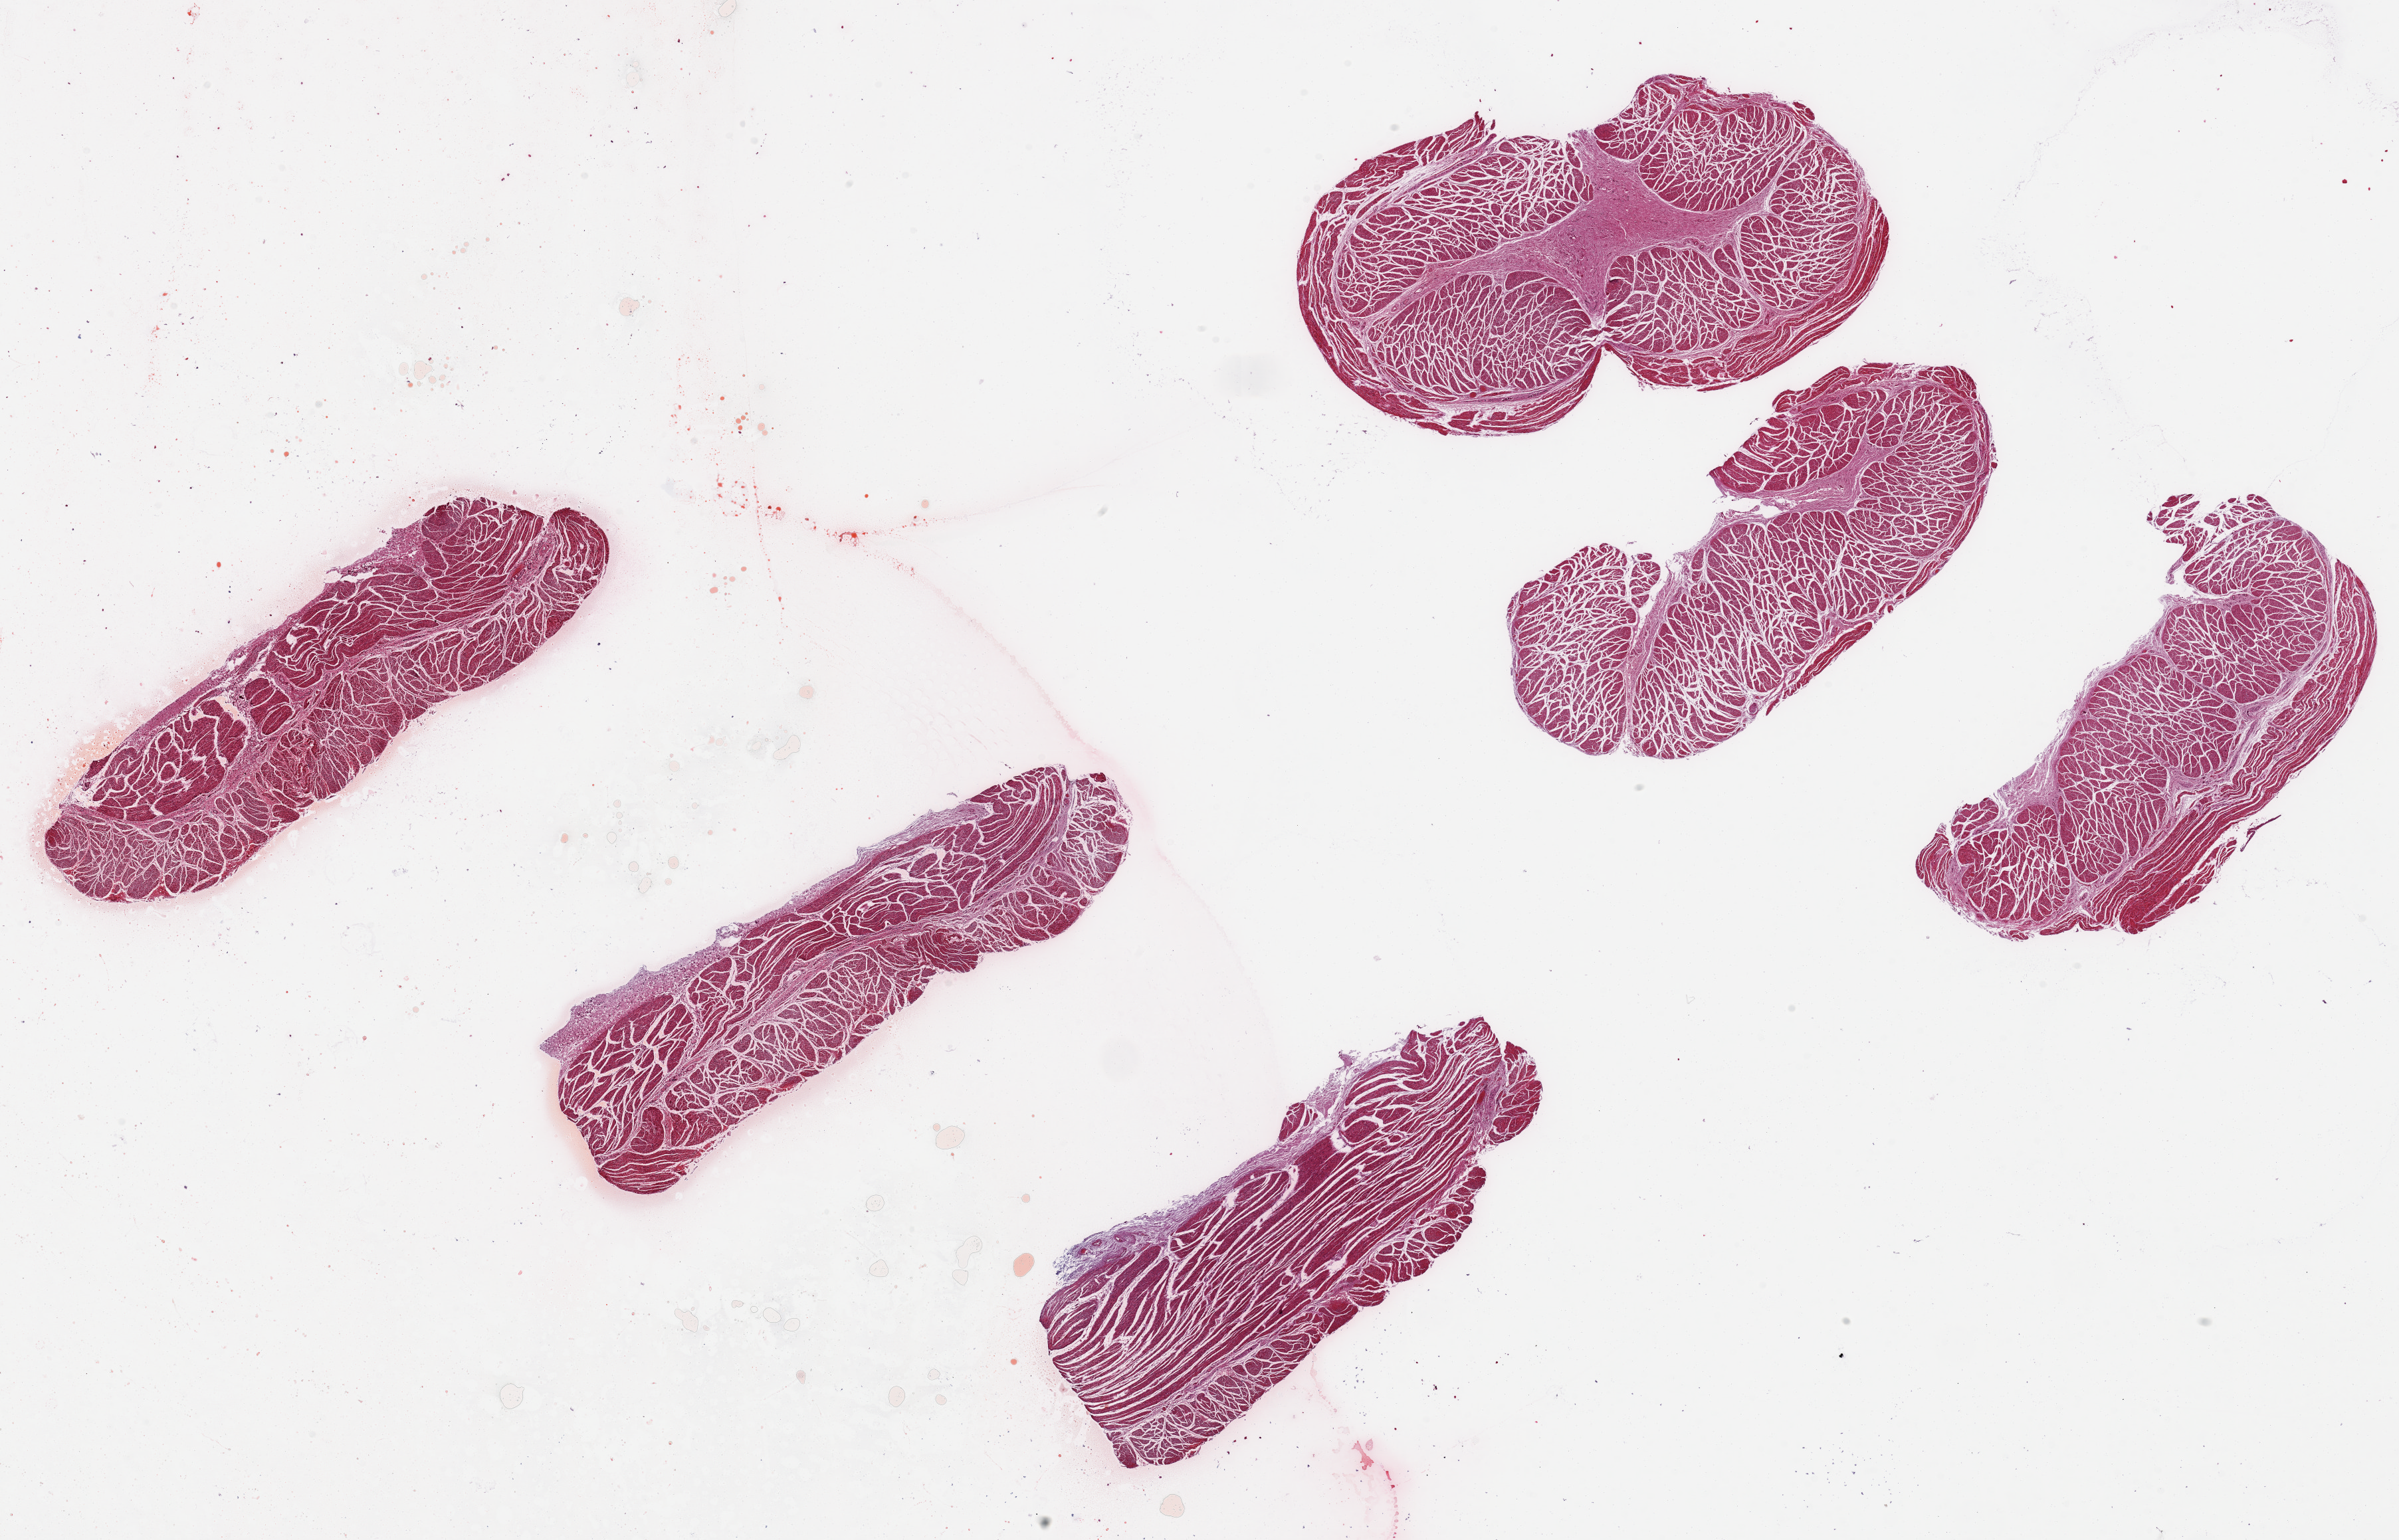
Digitized haematoxylin and eosin-stained section — shown as a low-resolution overview of the whole scanned area (about 28.5 x 18.3 mm), PAXgene-fixed, paraffin-embedded tissue, section of esophageal muscle (target tissue), donor tissue sample. Donor: male.
Pathologist's review note for this sample: 6 pieces up to 7x3 mm.